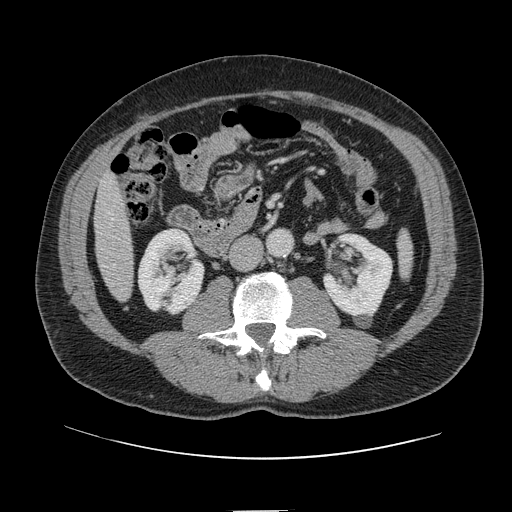
Contrast-enhanced abdominal CT, one axial slice; 120 kVp; intravenous contrast given; soft-tissue window (W 400 / L 40 HU); 2.5 mm slice thickness; 512 × 512 image matrix. Male patient, age 66 years. Case-level facts recorded for this patient, not image findings: diagnosis: colorectal cancer liver metastases, imaged before liver resection; multiple liver metastases: no; largest metastasis: 3.5 cm; disease in both lobes: no.
Outlined on this slice (outlined manually by an expert reader):
- liver: bounding box <95,176,132,300> (left, top, right, bottom; pixels)
- planned liver remnant (the part of the liver to remain after resection): <95,176,128,253>